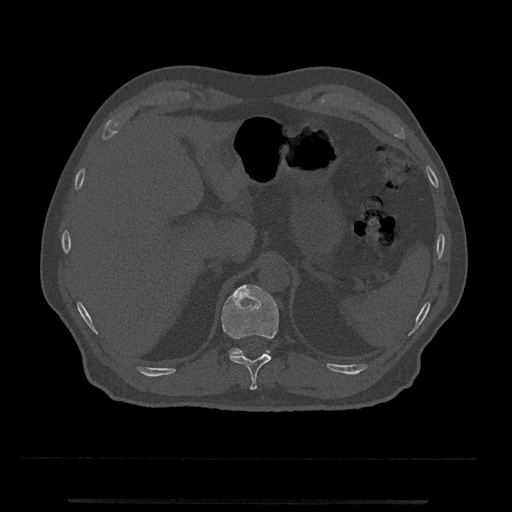
CT including the spine, one axial slice. Position 449 of 797 along the scan axis. Reconstruction kernel Br40s/3. Bone window (W 1800 / L 400 HU). 0.5 mm slice thickness. 512 × 512 image matrix, field of view 419 × 419 mm. Male patient, age 63 years. Case-level facts recorded for this patient, not image findings: primary cancer: prostate.
Outlined on this slice (semi-automatically segmented with operator editing):
- T11 vertebra: bounding box [x1, y1, x2, y2] px = [221, 285, 279, 390]
- T12 vertebra: [229, 348, 271, 356]